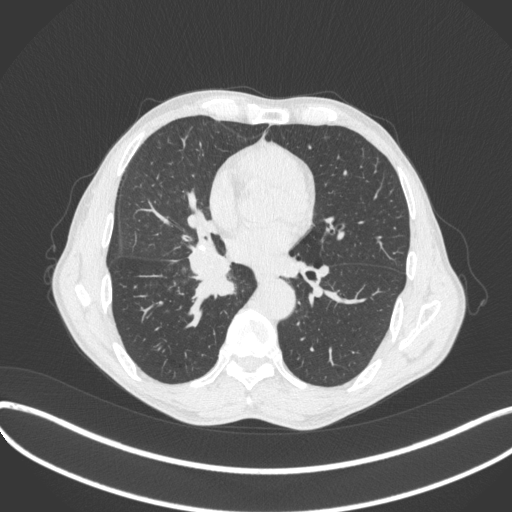
Chest CT, one axial slice; position 206 of 481 along the scan axis; reconstruction kernel B31f; 120 kVp; lung window (W 1500 / L -600 HU); 1 mm slice thickness; 512 × 512 image matrix, field of view 400 × 400 mm. Male patient, age 65 years. Case-level facts recorded for this patient, not image findings: clinical TNM (as recorded): T2a N0 M0.
Structures marked on this image (rectangle marked by the reading radiologist):
- lung tumour (recorded histology: squamous cell carcinoma): bounding box [x1, y1, x2, y2] px = [185, 239, 237, 303]